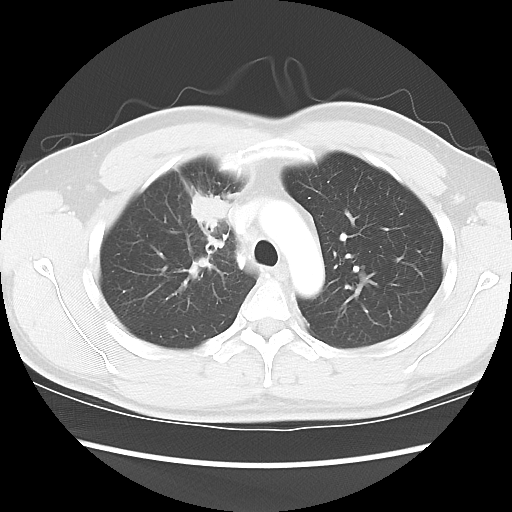
Chest CT, one axial slice. Slice 65 of 80 in the series (ordered by position). Reconstruction kernel LUNG. Lung window (W 1500 / L -600 HU). 512 × 512 image matrix, field of view 360 × 360 mm. Male patient, age 35 years. Case-level facts recorded for this patient, not image findings: clinical TNM (as recorded): T1c N1 M1b.
Outlined on this slice (bounding box drawn by a radiologist):
- lung tumour (recorded histology: adenocarcinoma): box from (x=184, y=189) to (x=234, y=239) px